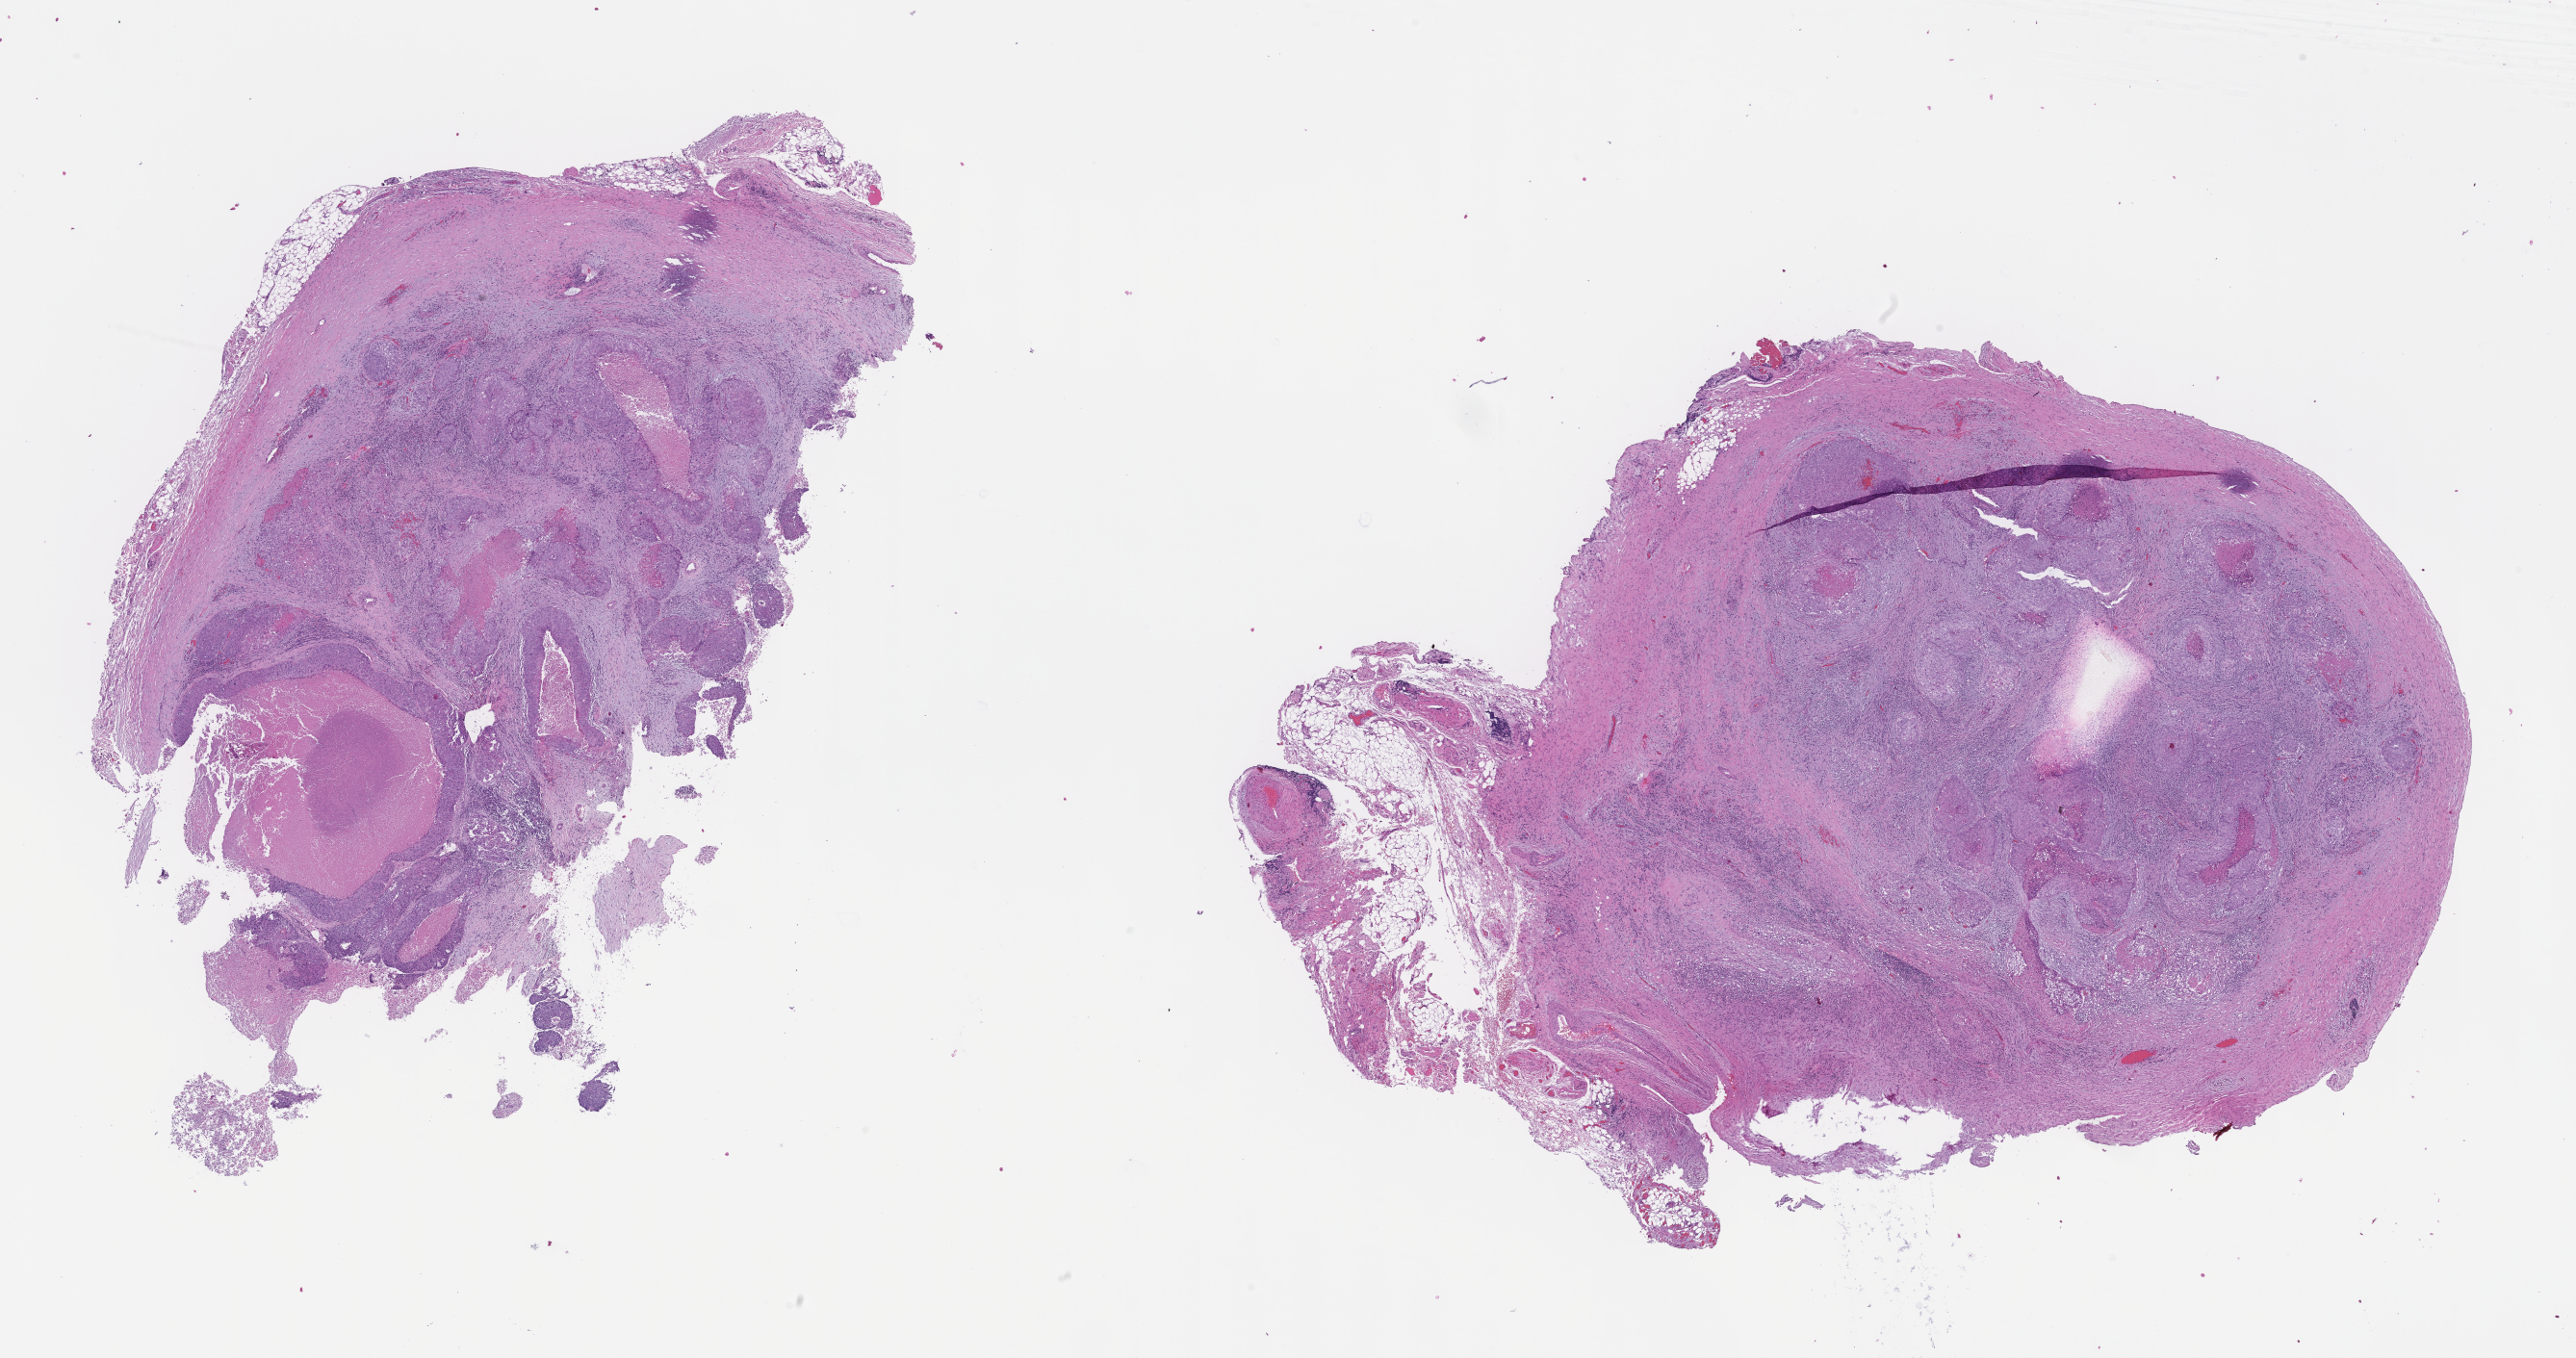
Whole-slide image, haematoxylin and eosin stain, low-resolution overview of the scanned area, about 21.6 x 11.4 mm; formalin-fixed, paraffin-embedded (FFPE) tissue; specimen time point: archival tissue. Patient: female.
This section: metastasis (sampled organ not recorded). Primary diagnosis of the patient: Non-Small Cell Lung Carcinoma.